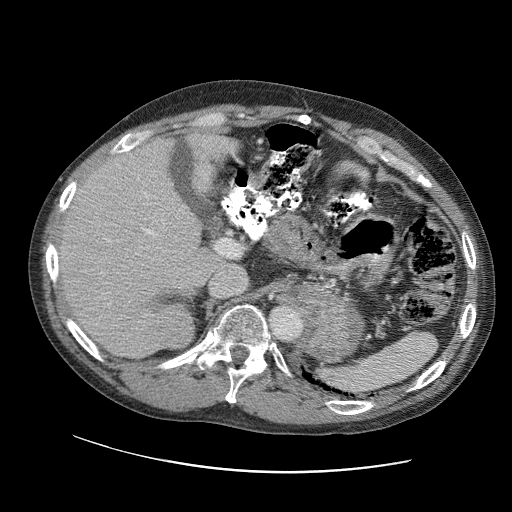
Contrast-enhanced abdominal CT (liver protocol), one axial slice; position 68 of 109 along the scan axis; reconstruction kernel STANDARD; 120 kVp; soft-tissue window (W 400 / L 40 HU); 2.5 mm slice thickness; 512 × 512 image matrix, field of view 400 × 400 mm. Case-level facts recorded for this patient, not image findings: diagnosis: hepatocellular carcinoma (patient treated with transarterial chemoembolisation; whether this scan precedes or follows treatment is not stated here); TNM stage (as recorded): Stage-IIIC; Child-Pugh class: B; tumour differentiation: well differentiated; tumour nodularity: uninodular.
Annotated regions visible in this slice (semi-automatic segmentation, software-assisted and operator-edited):
- liver parenchyma outside the tumour (the mass and vessels are separate outlines, so this box may not span the whole liver): bounding box [x1, y1, x2, y2] px = [54, 136, 220, 358]
- mass: [161, 311, 193, 348]
- liver vessels: [103, 144, 199, 306]